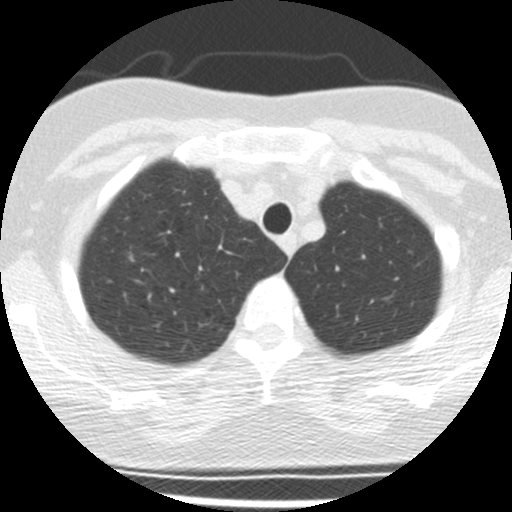
Low-dose screening chest CT, axial slice. Baseline annual screen. Lung window (W 1500 / L -600 HU). Slice 37 of 190 in the series. Female participant, aged 56 years at enrolment.
Expert reader's lesion annotation, bounding box (x1, y1, x2, y2) in pixels: (103, 231, 144, 271). Screening reader's record for this exam (one nodule recorded; not confirmed to be the boxed lesion): non-calcified nodule or mass ≥4 mm, right upper lobe, 6 × 6 mm, smooth margins, soft tissue attenuation. Official screen result: positive, change unspecified: nodule(s) >= 4 mm or enlarging nodule(s), mass(es), or other non-specific abnormalities suspicious for lung cancer. Lung cancer was diagnosed 281 days after this screen: small cell carcinoma, NOS, right upper lobe, stage IIIB (AJCC 6th edition).